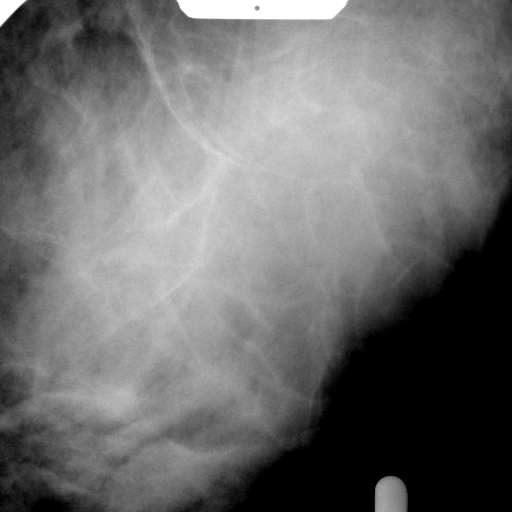
Spot-compression mammographic view.
Pathology recorded for this patient (not read from this image): pathology diagnosis: benign fibroadenoma (right breast); pathology report notes: RIGHT BREAST CALCIFICATION WITH NEEDLE LOCATION: FIBROADENOMA (1.9CM). REMAINING BREAST TISSUE WITH ADENOSIS, FOCAL FIBROADENOMATOUS CHANGES, APOCRINE METAPLASIA, FIBROCYSTIC CHANGES, SMALL INTRADUCTAL PAPILLOMAS, AND USUAL TYPE DUCTAL HYPERPLASIA. MICROCALCIFICATIONS ASSOCIATED WITH BENIGN BREAST TISSUE ARE IDENTIFIED. NO IN-SITU OR INVASIVE CARCINOMA.